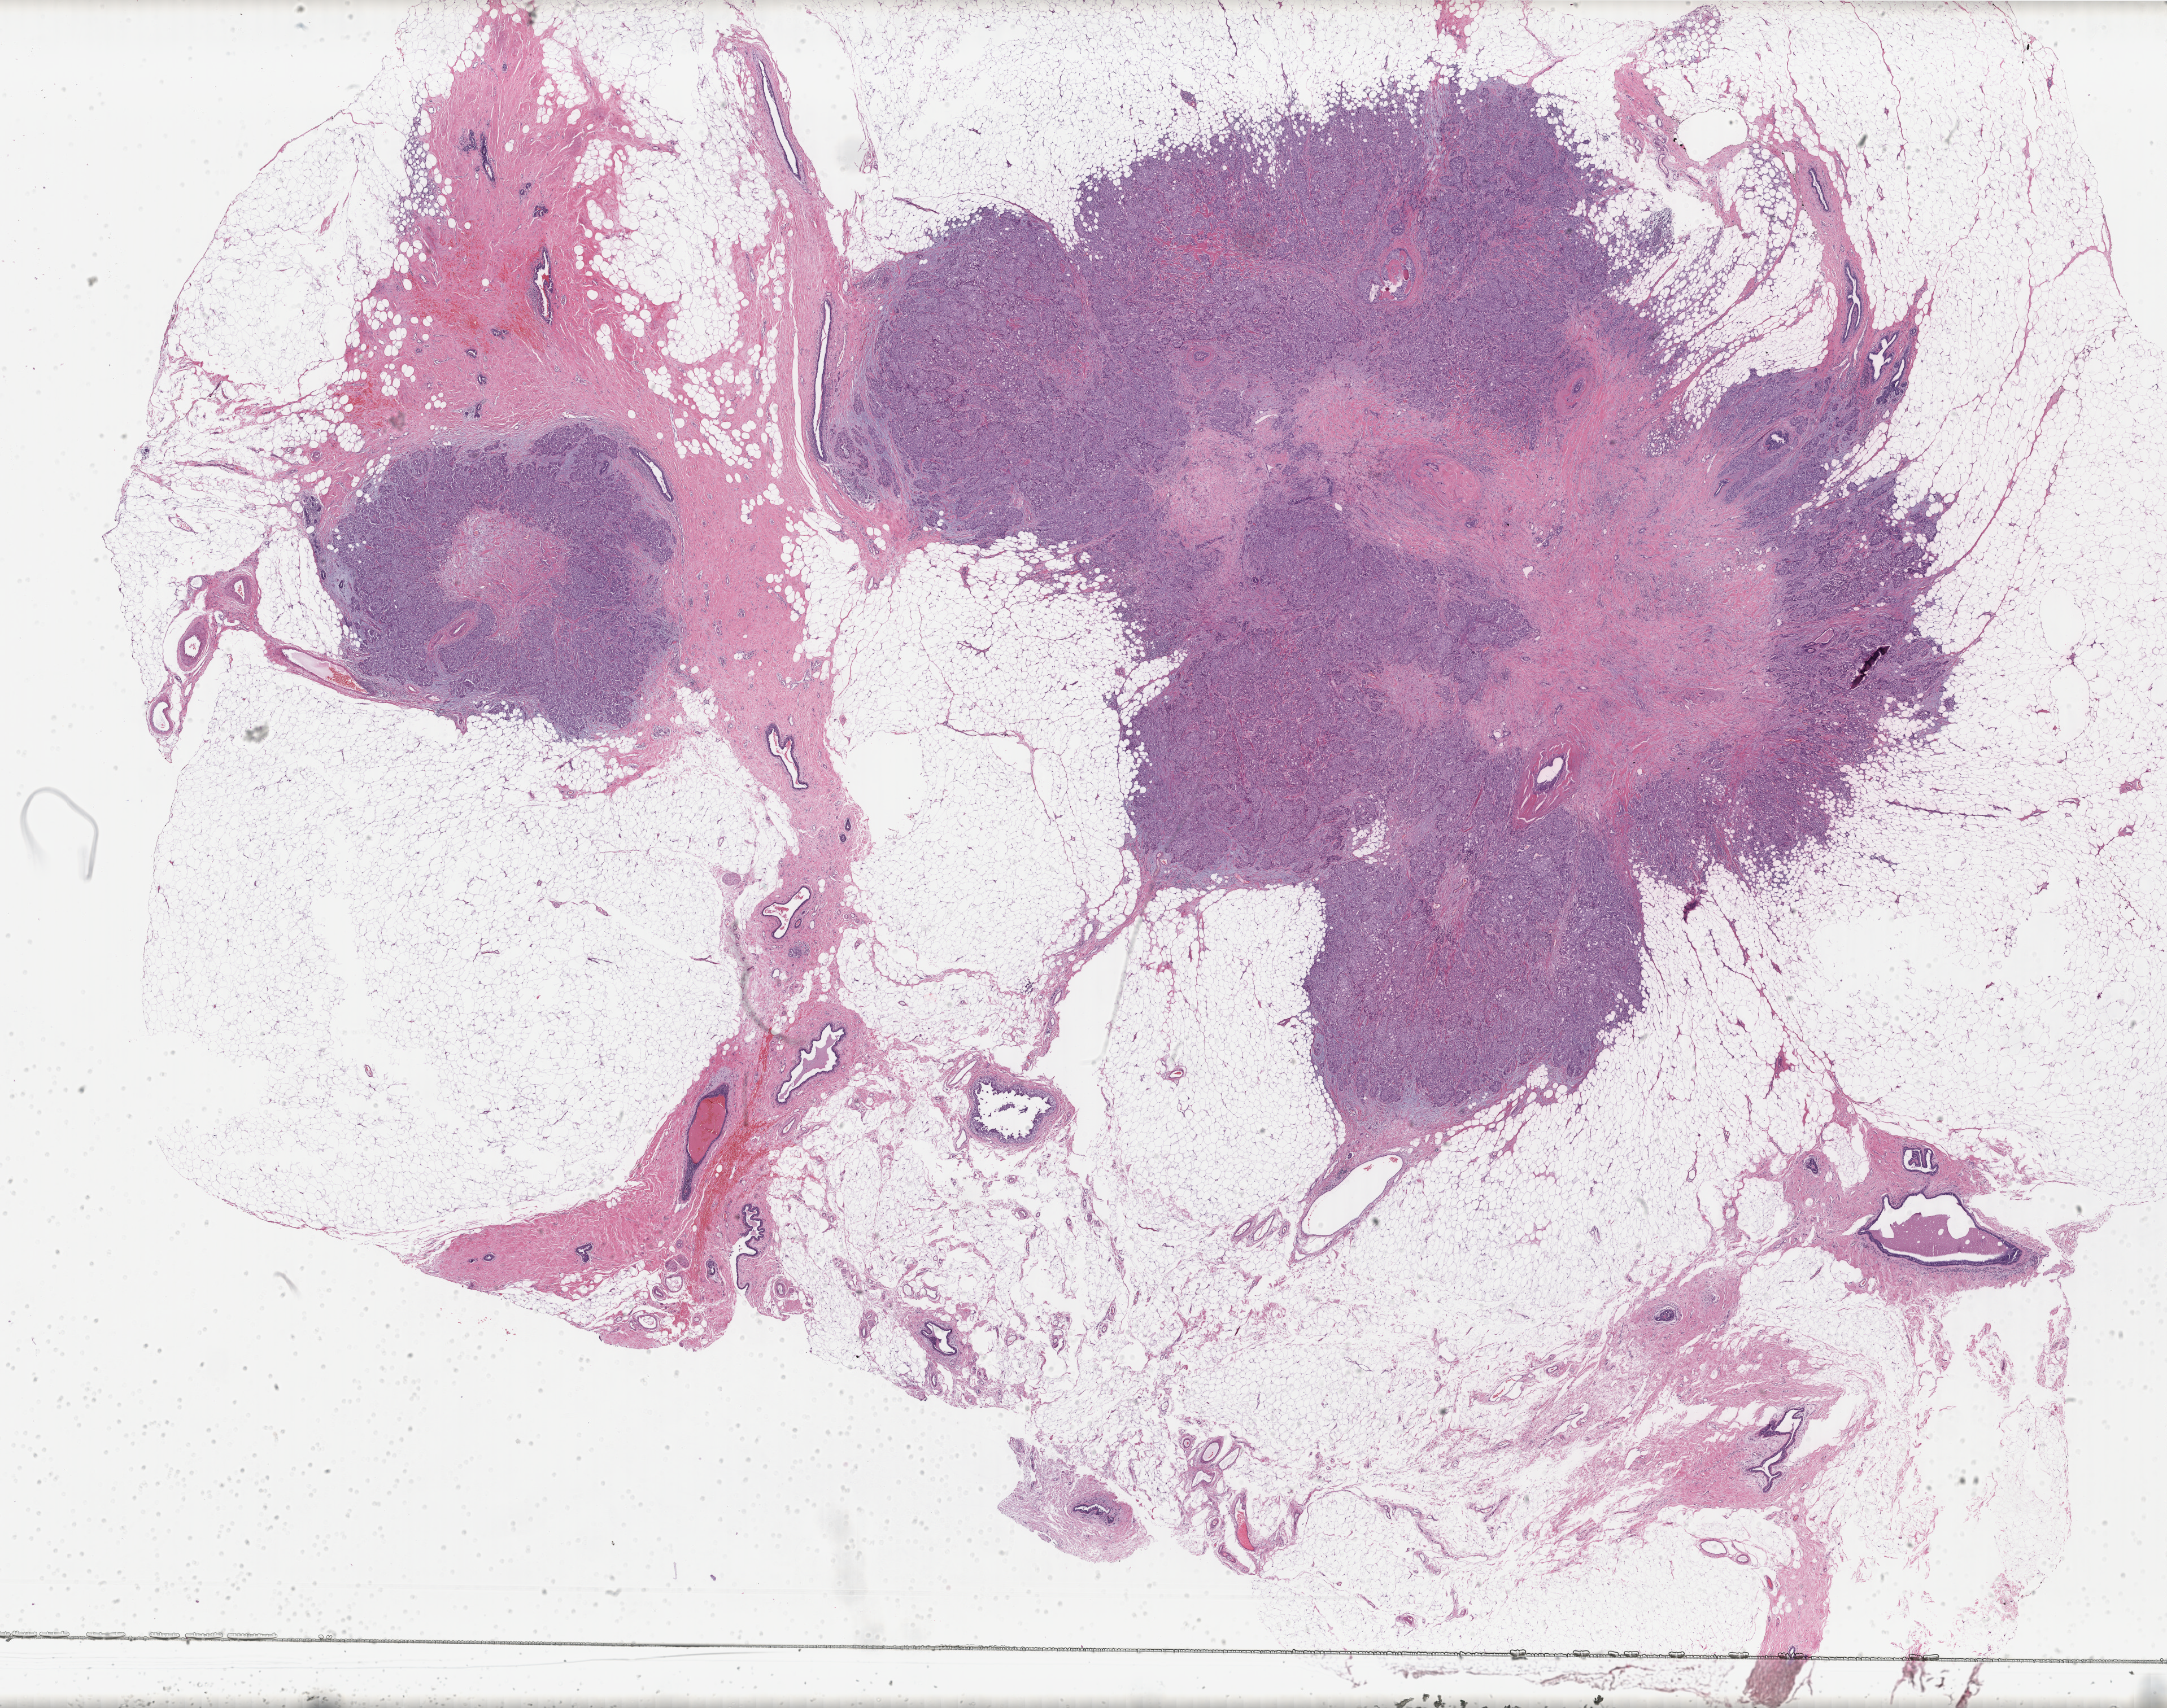
Digitized H&E tissue section (whole slide), shown as a low-resolution overview of the whole scanned area (about 30.5 x 24.0 mm, acquisition: 40x scan), formalin-fixed paraffin-embedded (FFPE) diagnostic section, sample: primary tumour, breast. Patient: female, age at initial diagnosis 66 years.
Histologic diagnosis: Infiltrating duct carcinoma, NOS.